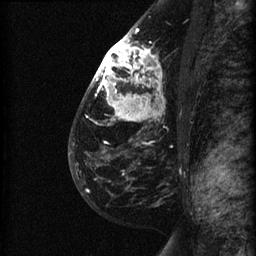
Breast MRI (dynamic contrast-enhanced), one sagittal slice. Slice 41 of 60 in the series (ordered by position). Dynamic contrast-enhanced series, image 2 of 3 at this slice position (ordered by acquisition). 1.5 T. TE 4.2 ms, TR 22.7 ms. 256 × 256 image matrix, field of view 180 × 180 mm. Female patient, age 48 years. Case-level facts recorded for this patient, not image findings: setting: breast cancer imaged before/during neoadjuvant chemotherapy; receptor status: triple-negative.
Outlined on this slice (semi-automatically segmented with operator editing):
- analysis volume of interest (the breast-tissue region the enhancement analysis was run in; not a lesion): bounding box (x1, y1, x2, y2) in pixels: (89, 27, 189, 180)
- tumour enhancement mask (voxels above the 90 % enhancement threshold inside the analysis volume of interest): (93, 28, 161, 120)